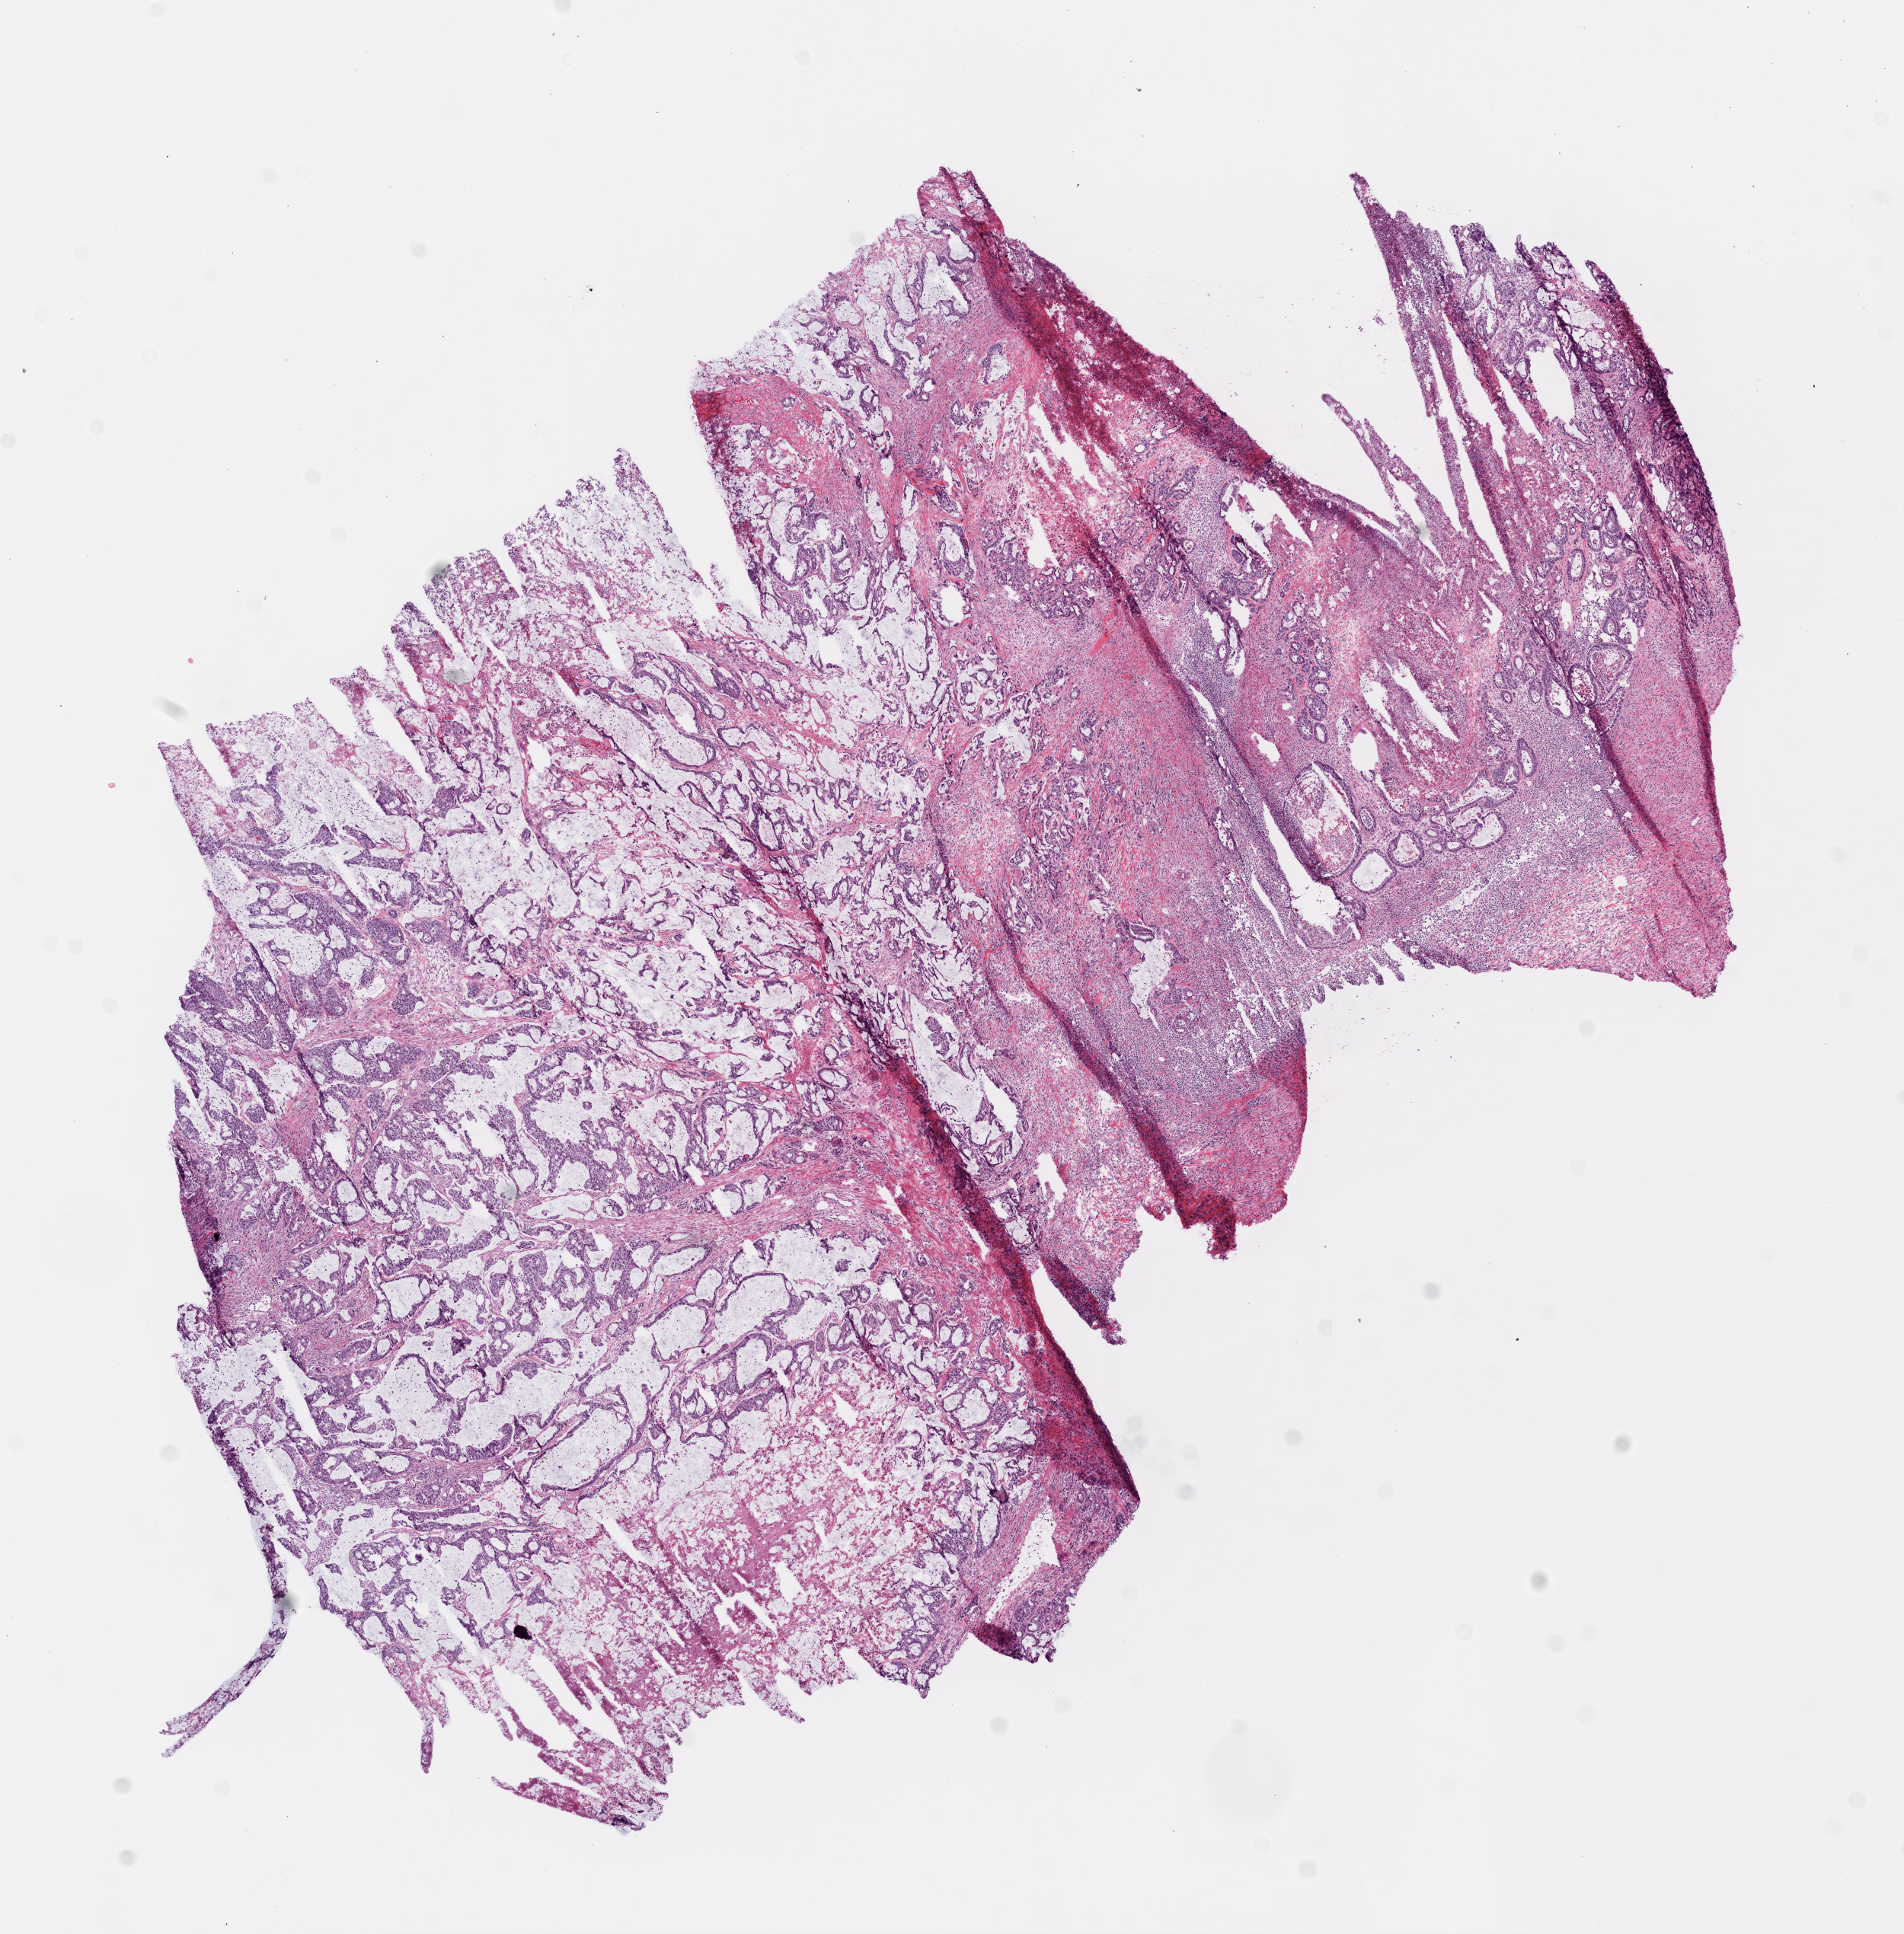
Whole-slide histology image, H&E-stained, low-resolution overview of the scanned area, about 10.0 x 10.2 mm; frozen section; colon, primary tumour sample. Male, age 71 years at initial diagnosis. Composition of this section per pathologist review: tumour cells 80%, tumour nuclei 80%, normal cells 0%, stromal cells 15%, necrosis 5%.
* TNM: T3 N2 M1
* AJCC pathologic stage: IV
* diagnosis: Mucinous adenocarcinoma